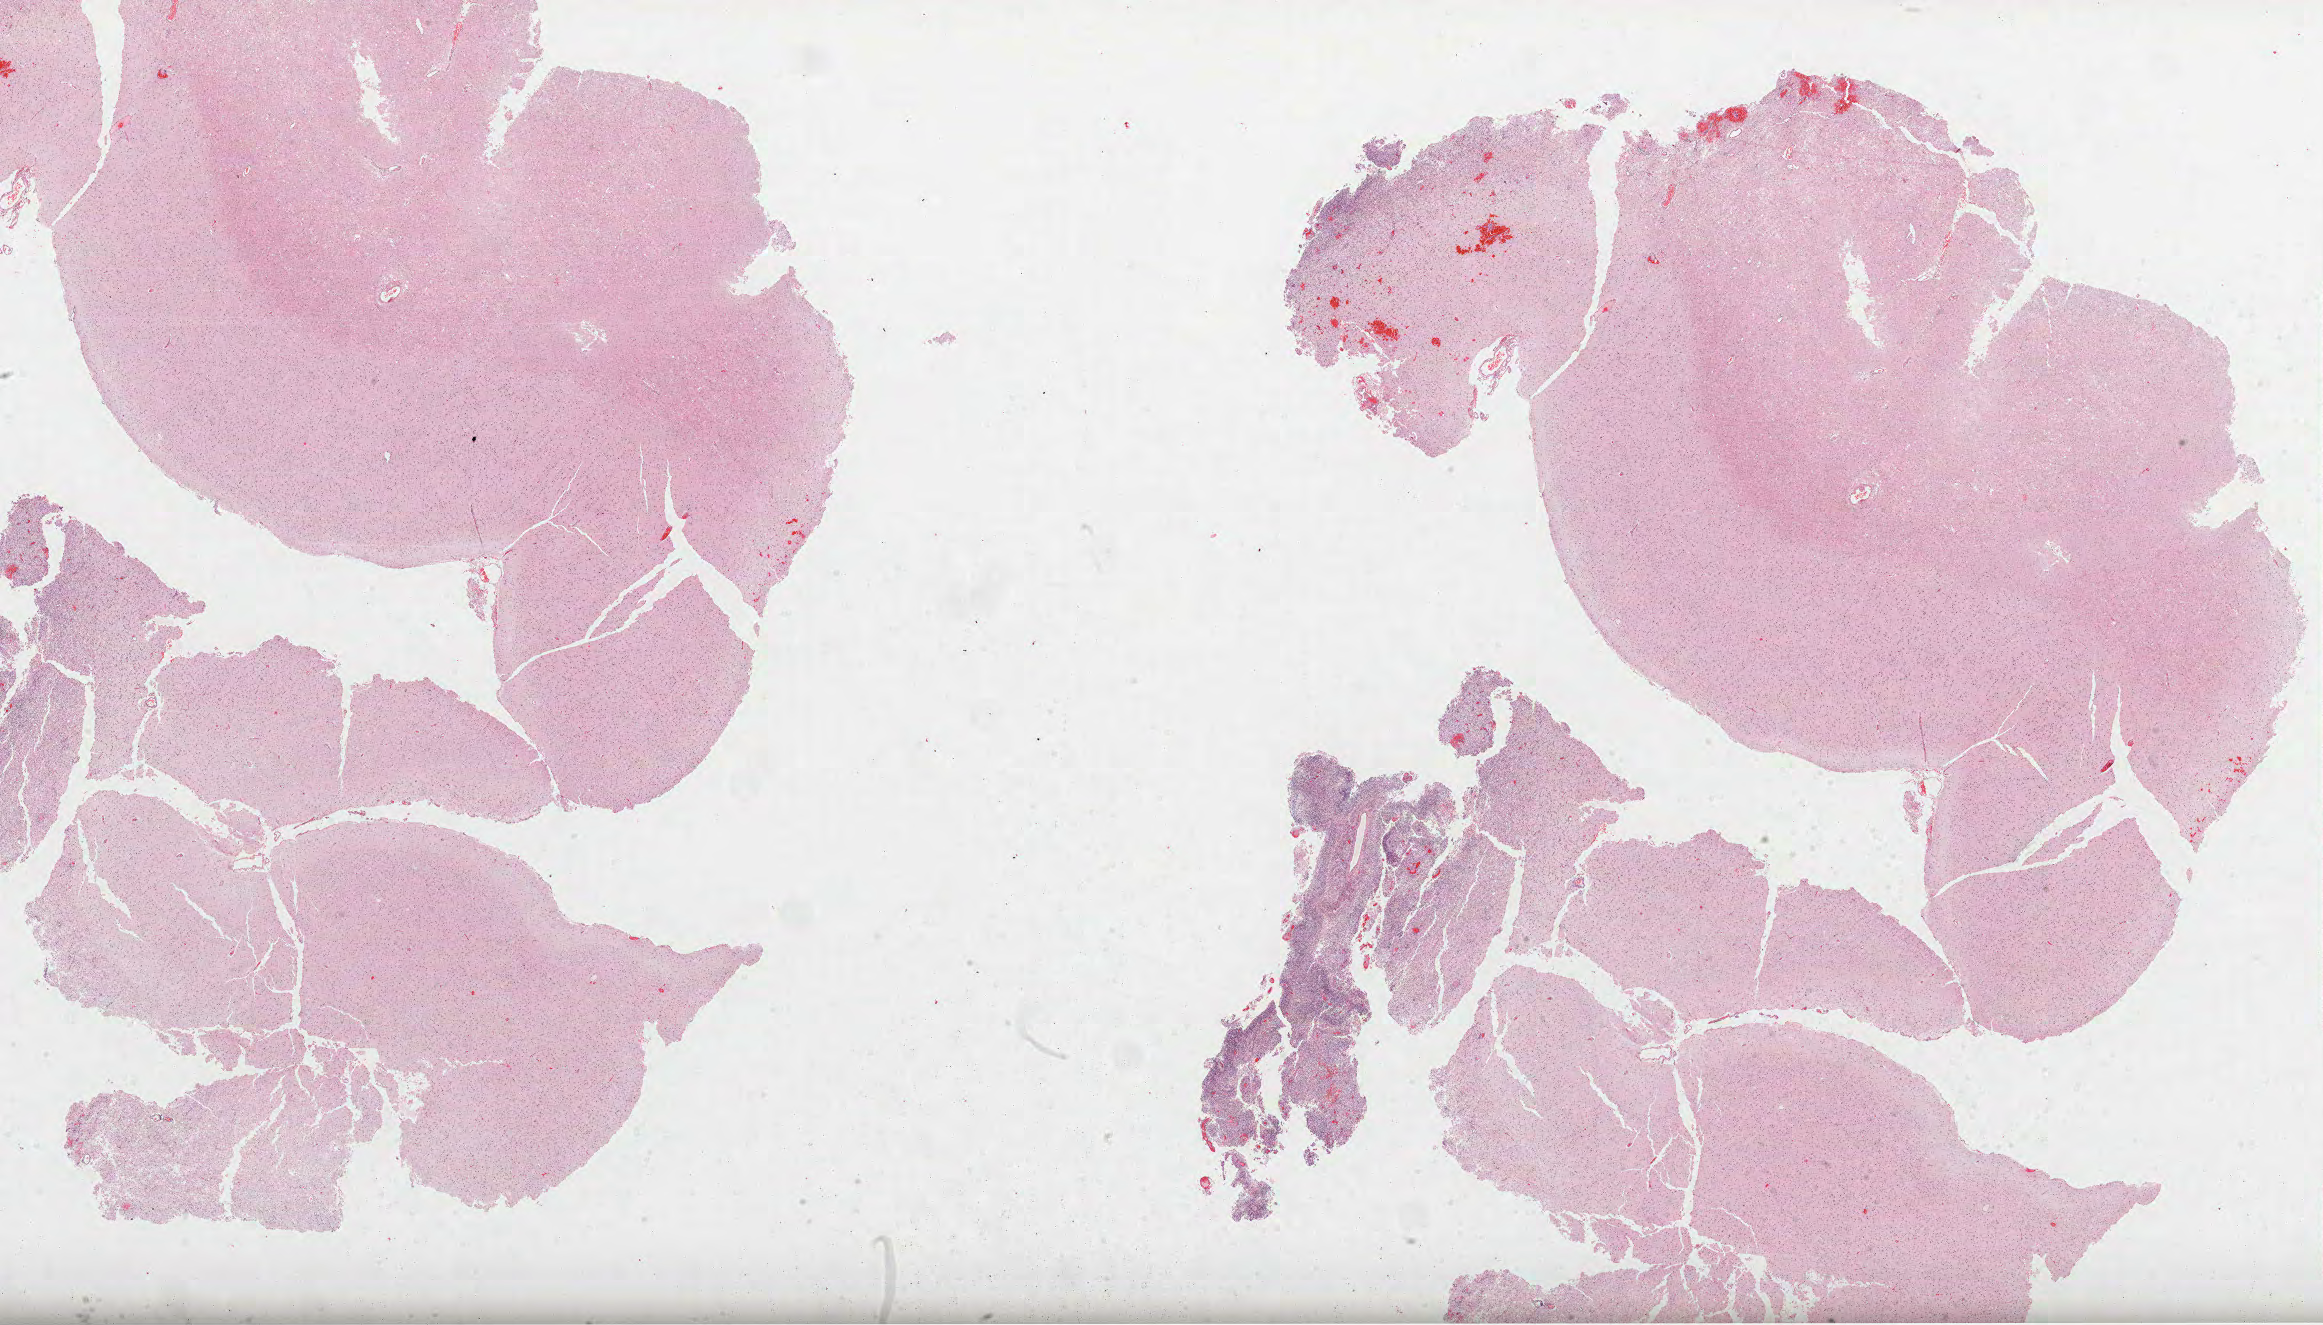
Whole-slide histology image, Hematoxylin and eosin (H&E) stained, shown as a low-resolution overview of the whole scanned area (about 37.5 x 21.4 mm, slide scanned at 40x). FFPE section. Sample: primary tumour, brain. Male patient; age at initial diagnosis 56 years.
Pathologic diagnosis: Glioblastoma.